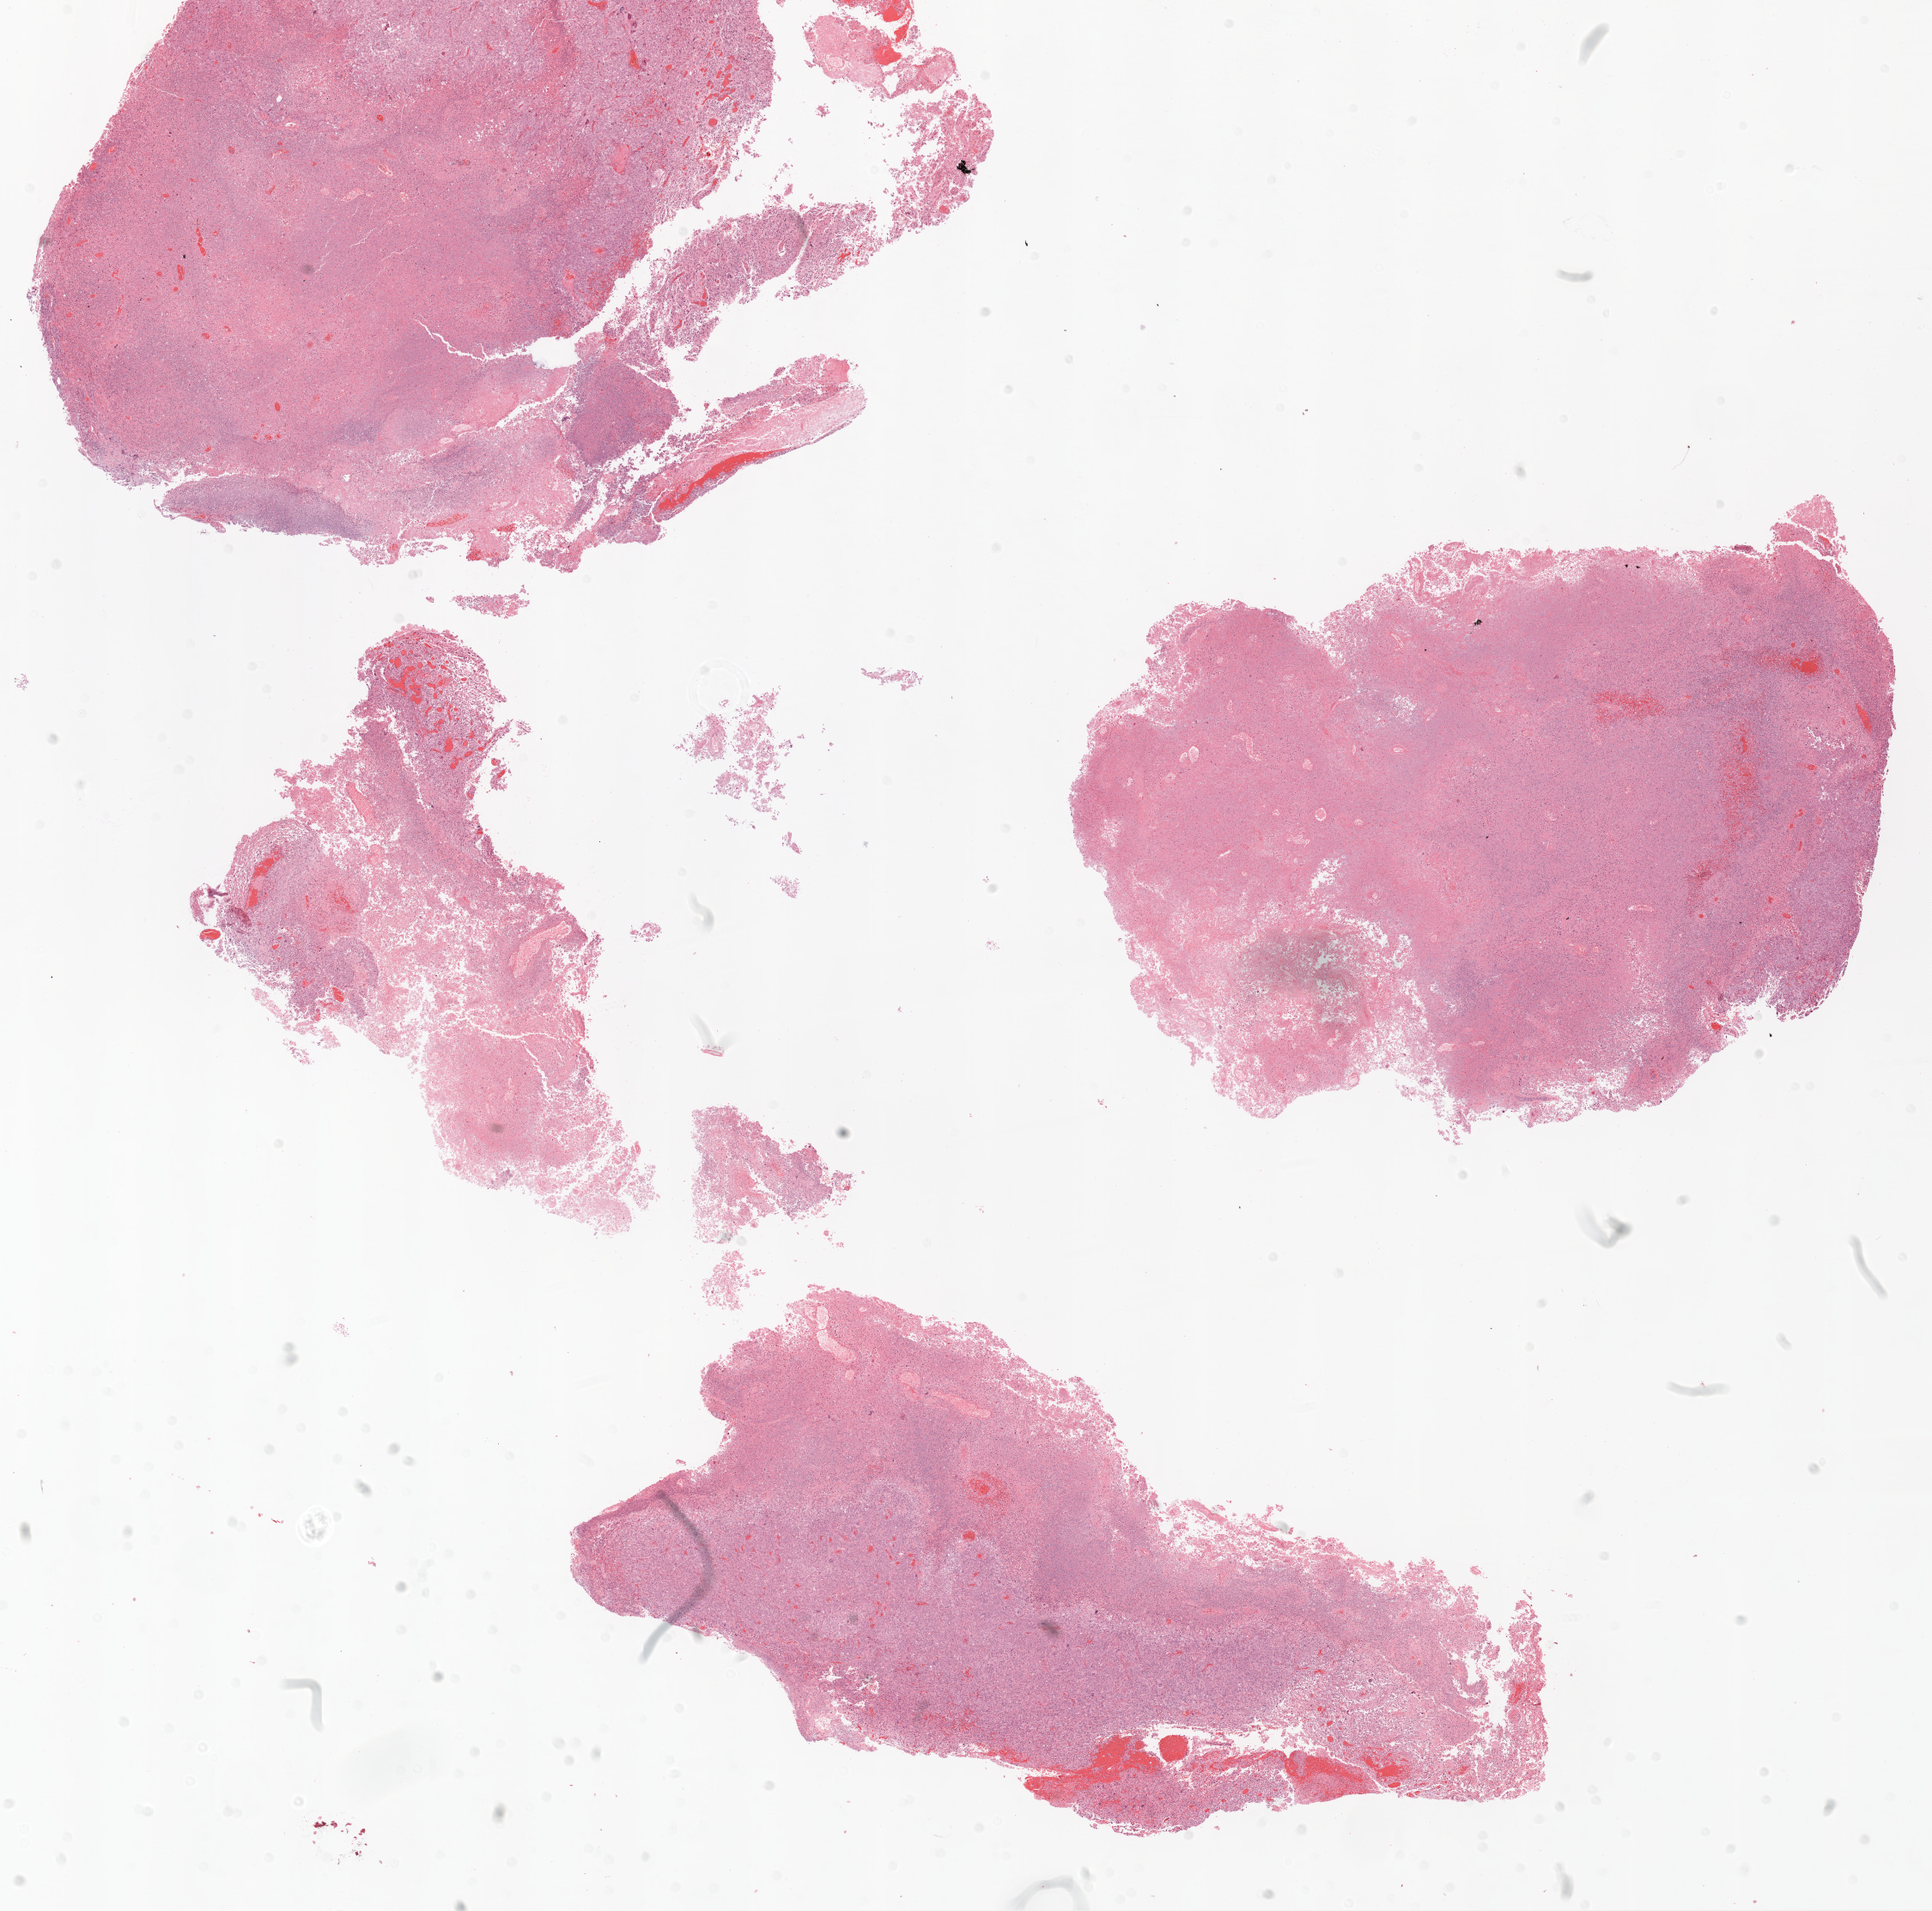
Digitized Hematoxylin and eosin (H&E) stained tissue section (whole slide), low-resolution overview of the scanned area, about 18.1 x 17.9 mm (from a 20x scan), FFPE section, sample: primary tumour, brain. Patient: male, age at initial diagnosis 34 years.
Pathologic diagnosis: Glioblastoma.